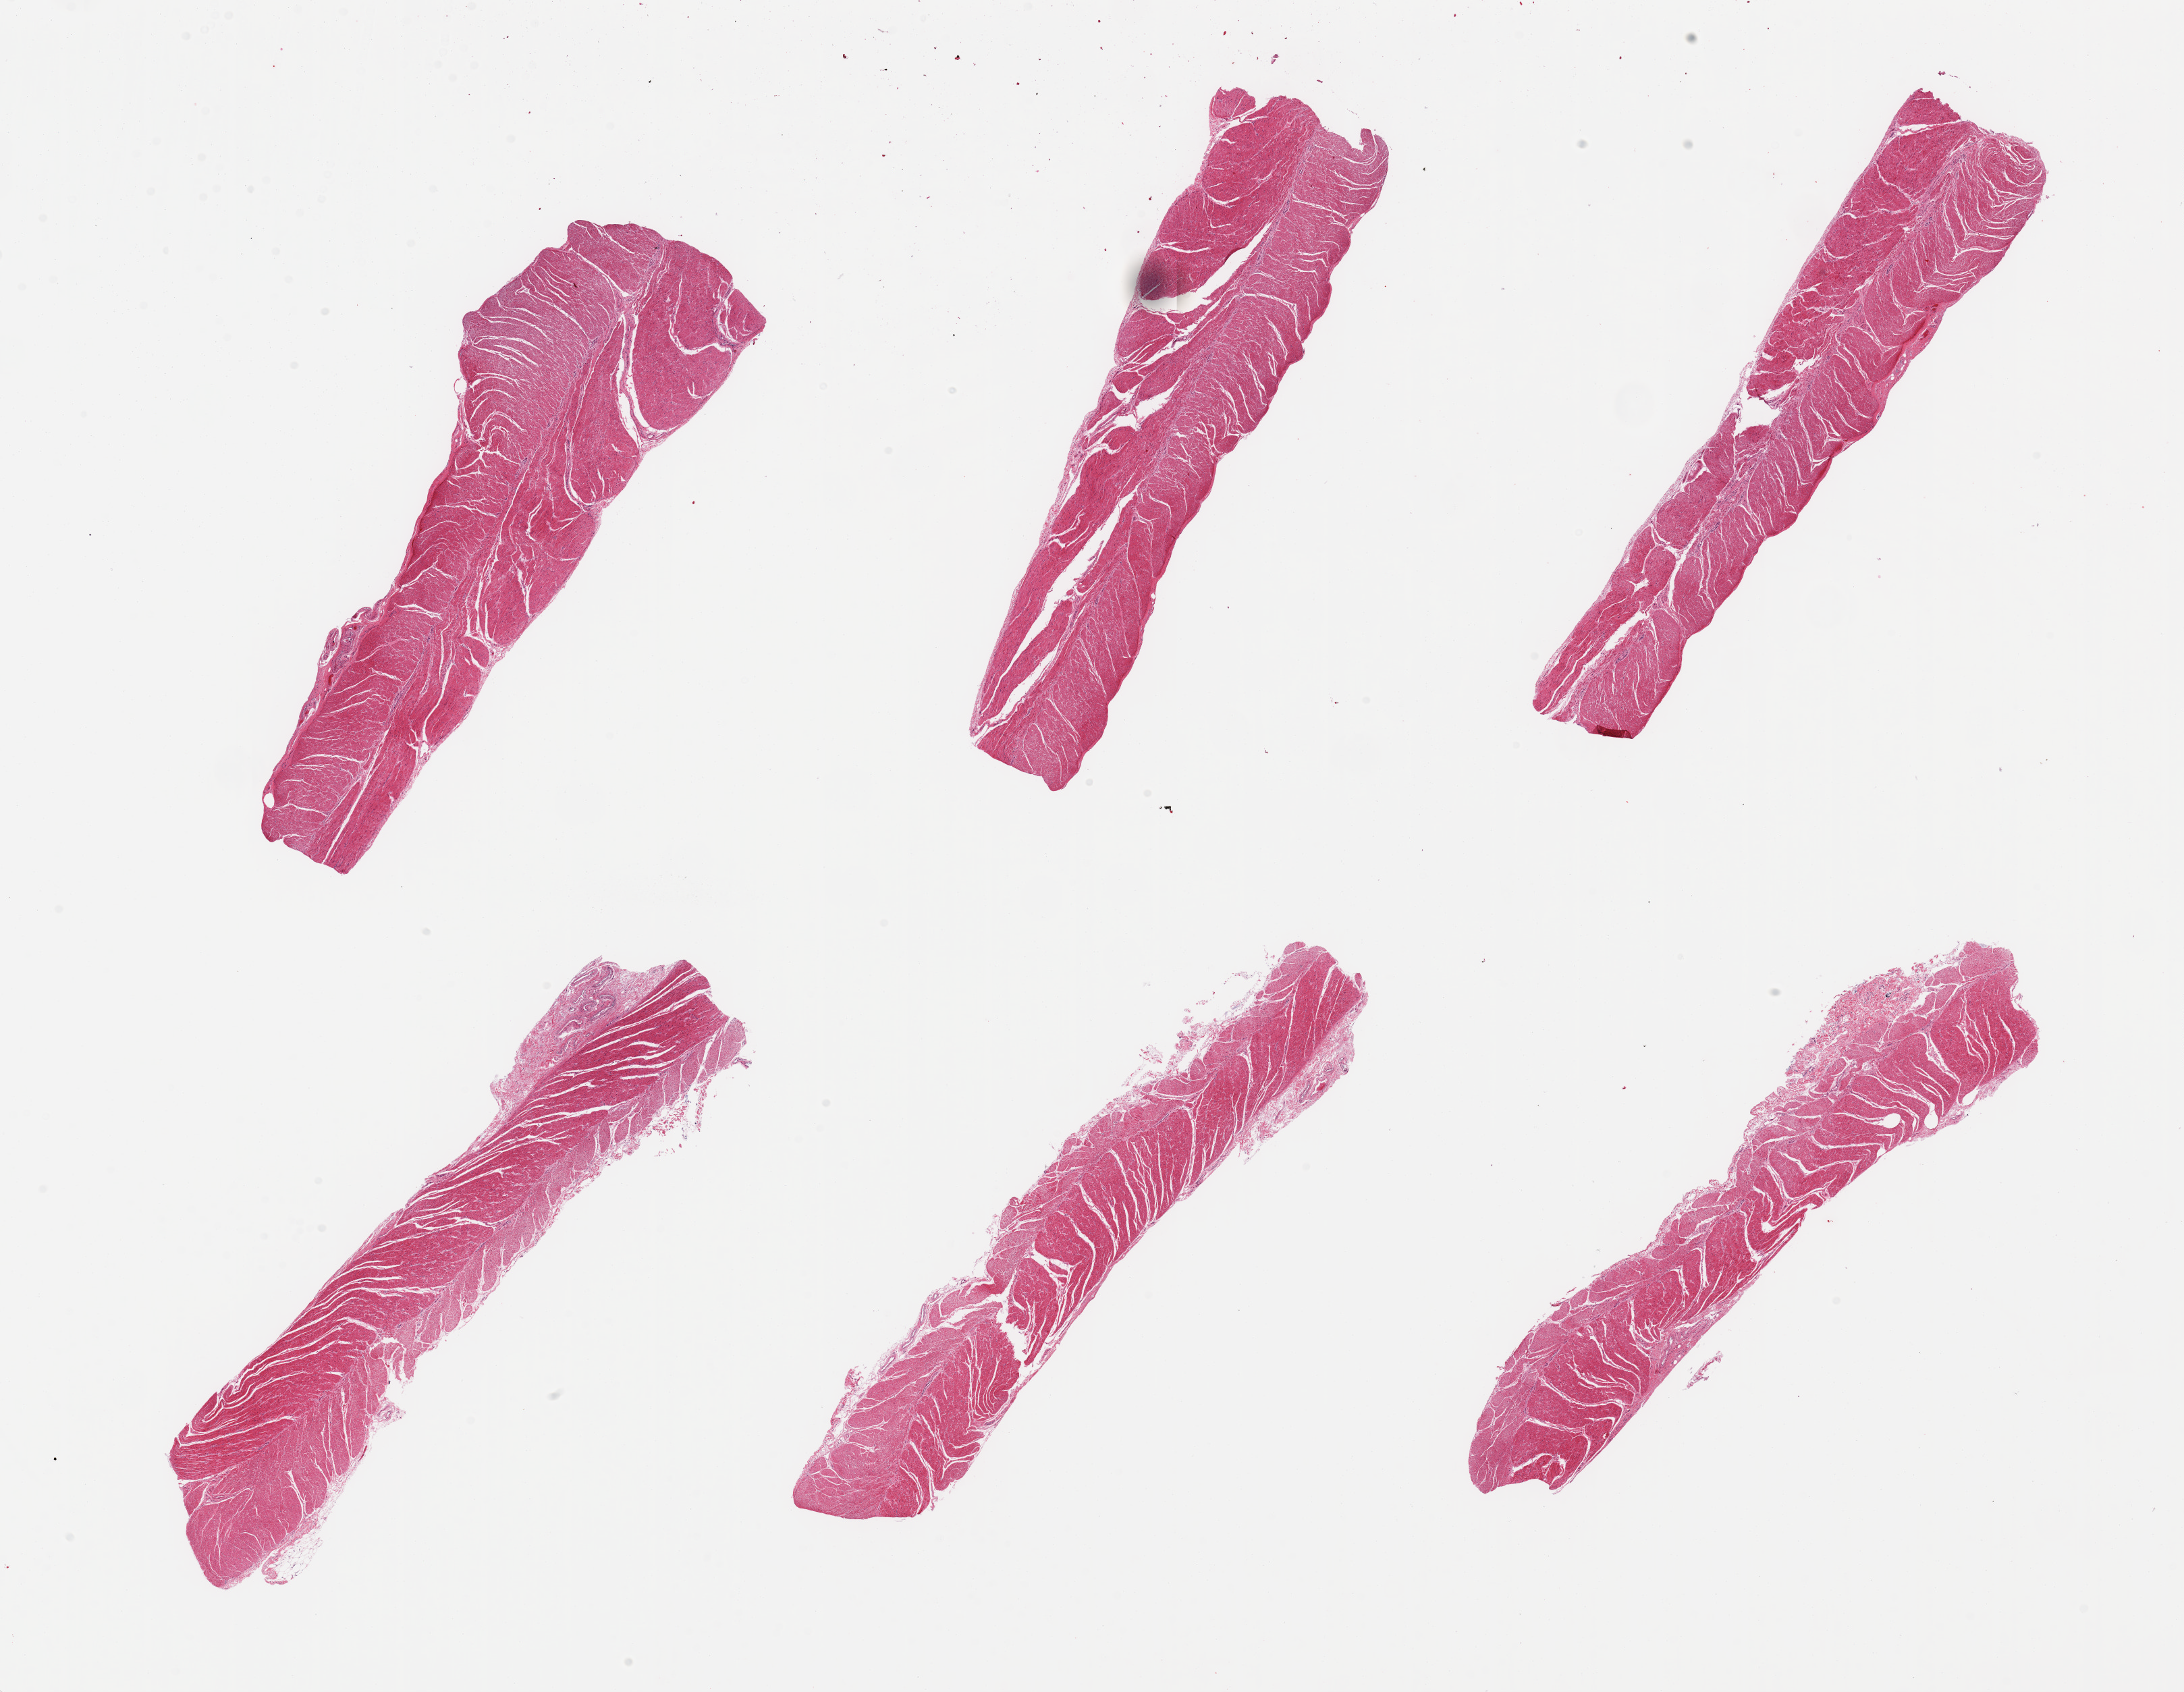
H&E whole-slide image, brightfield — a low-resolution overview of the entire scanned area, about 25.6 x 19.8 mm (from a 20x scan). PAXgene-fixed, paraffin-embedded tissue. Target tissue: sigmoid colon. Donor tissue sample.
Review note (as recorded): 6 pieces; well dissected muscularis.